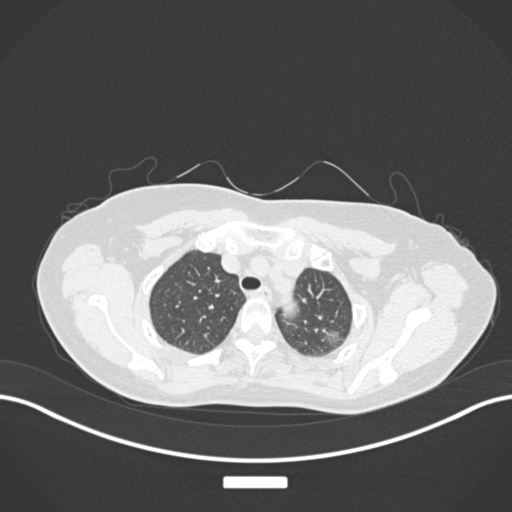
Chest CT, one axial slice. Position 141 of 181 along the scan axis. 120 kVp. Lung window (W 1500 / L -600 HU). 1 mm slice thickness. 512 × 512 image matrix, field of view 400 × 400 mm. Patient: female, 58 years. Case-level facts recorded for this patient, not image findings: clinical TNM (as recorded): T1c N0 M0.
Annotated regions visible in this slice (rectangle marked by the reading radiologist):
- lung tumour (recorded histology: adenocarcinoma): bounding box <319,325,341,346> (left, top, right, bottom; pixels)